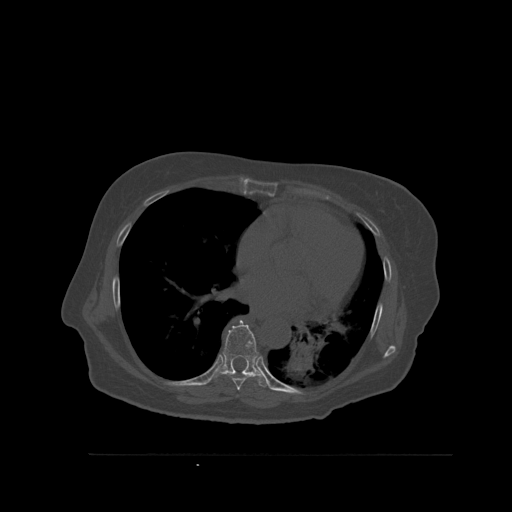
CT including the spine, one axial slice; slice 356 of 527 in the series (ordered by position); bone window (W 1800 / L 400 HU); 1.5 mm slice thickness; 512 × 512 image matrix, field of view 470 × 470 mm. Patient: female, 73 years. From the clinical record (not read from this slice): primary cancer: breast; vertebrae with lytic lesions (as recorded): L2.
Structures marked on this image (semi-automatic segmentation, software-assisted and operator-edited):
- T7 vertebra: bounding box [x1, y1, x2, y2] px = [229, 374, 256, 391]
- T8 vertebra: [210, 320, 268, 388]